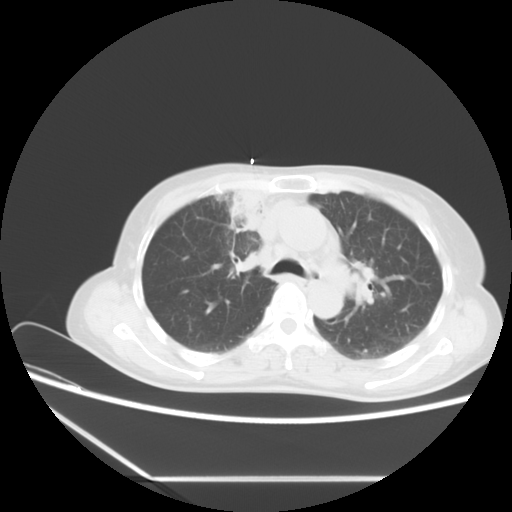
Chest CT, one axial slice. Slice 14 of 16 in the series (ordered by position). Reconstruction kernel STANDARD. 120 kVp. Lung window (W 1500 / L -600 HU). 5 mm slice thickness. 512 × 512 image matrix, field of view 350 × 350 mm. Female patient, age 63 years. From the clinical record (not read from this slice): clinical TNM (as recorded): T2b N1 M0.
Annotated regions visible in this slice (bounding box drawn by a radiologist):
- lung tumour (recorded histology: adenocarcinoma): bounding box [x1, y1, x2, y2] px = [226, 182, 262, 234]